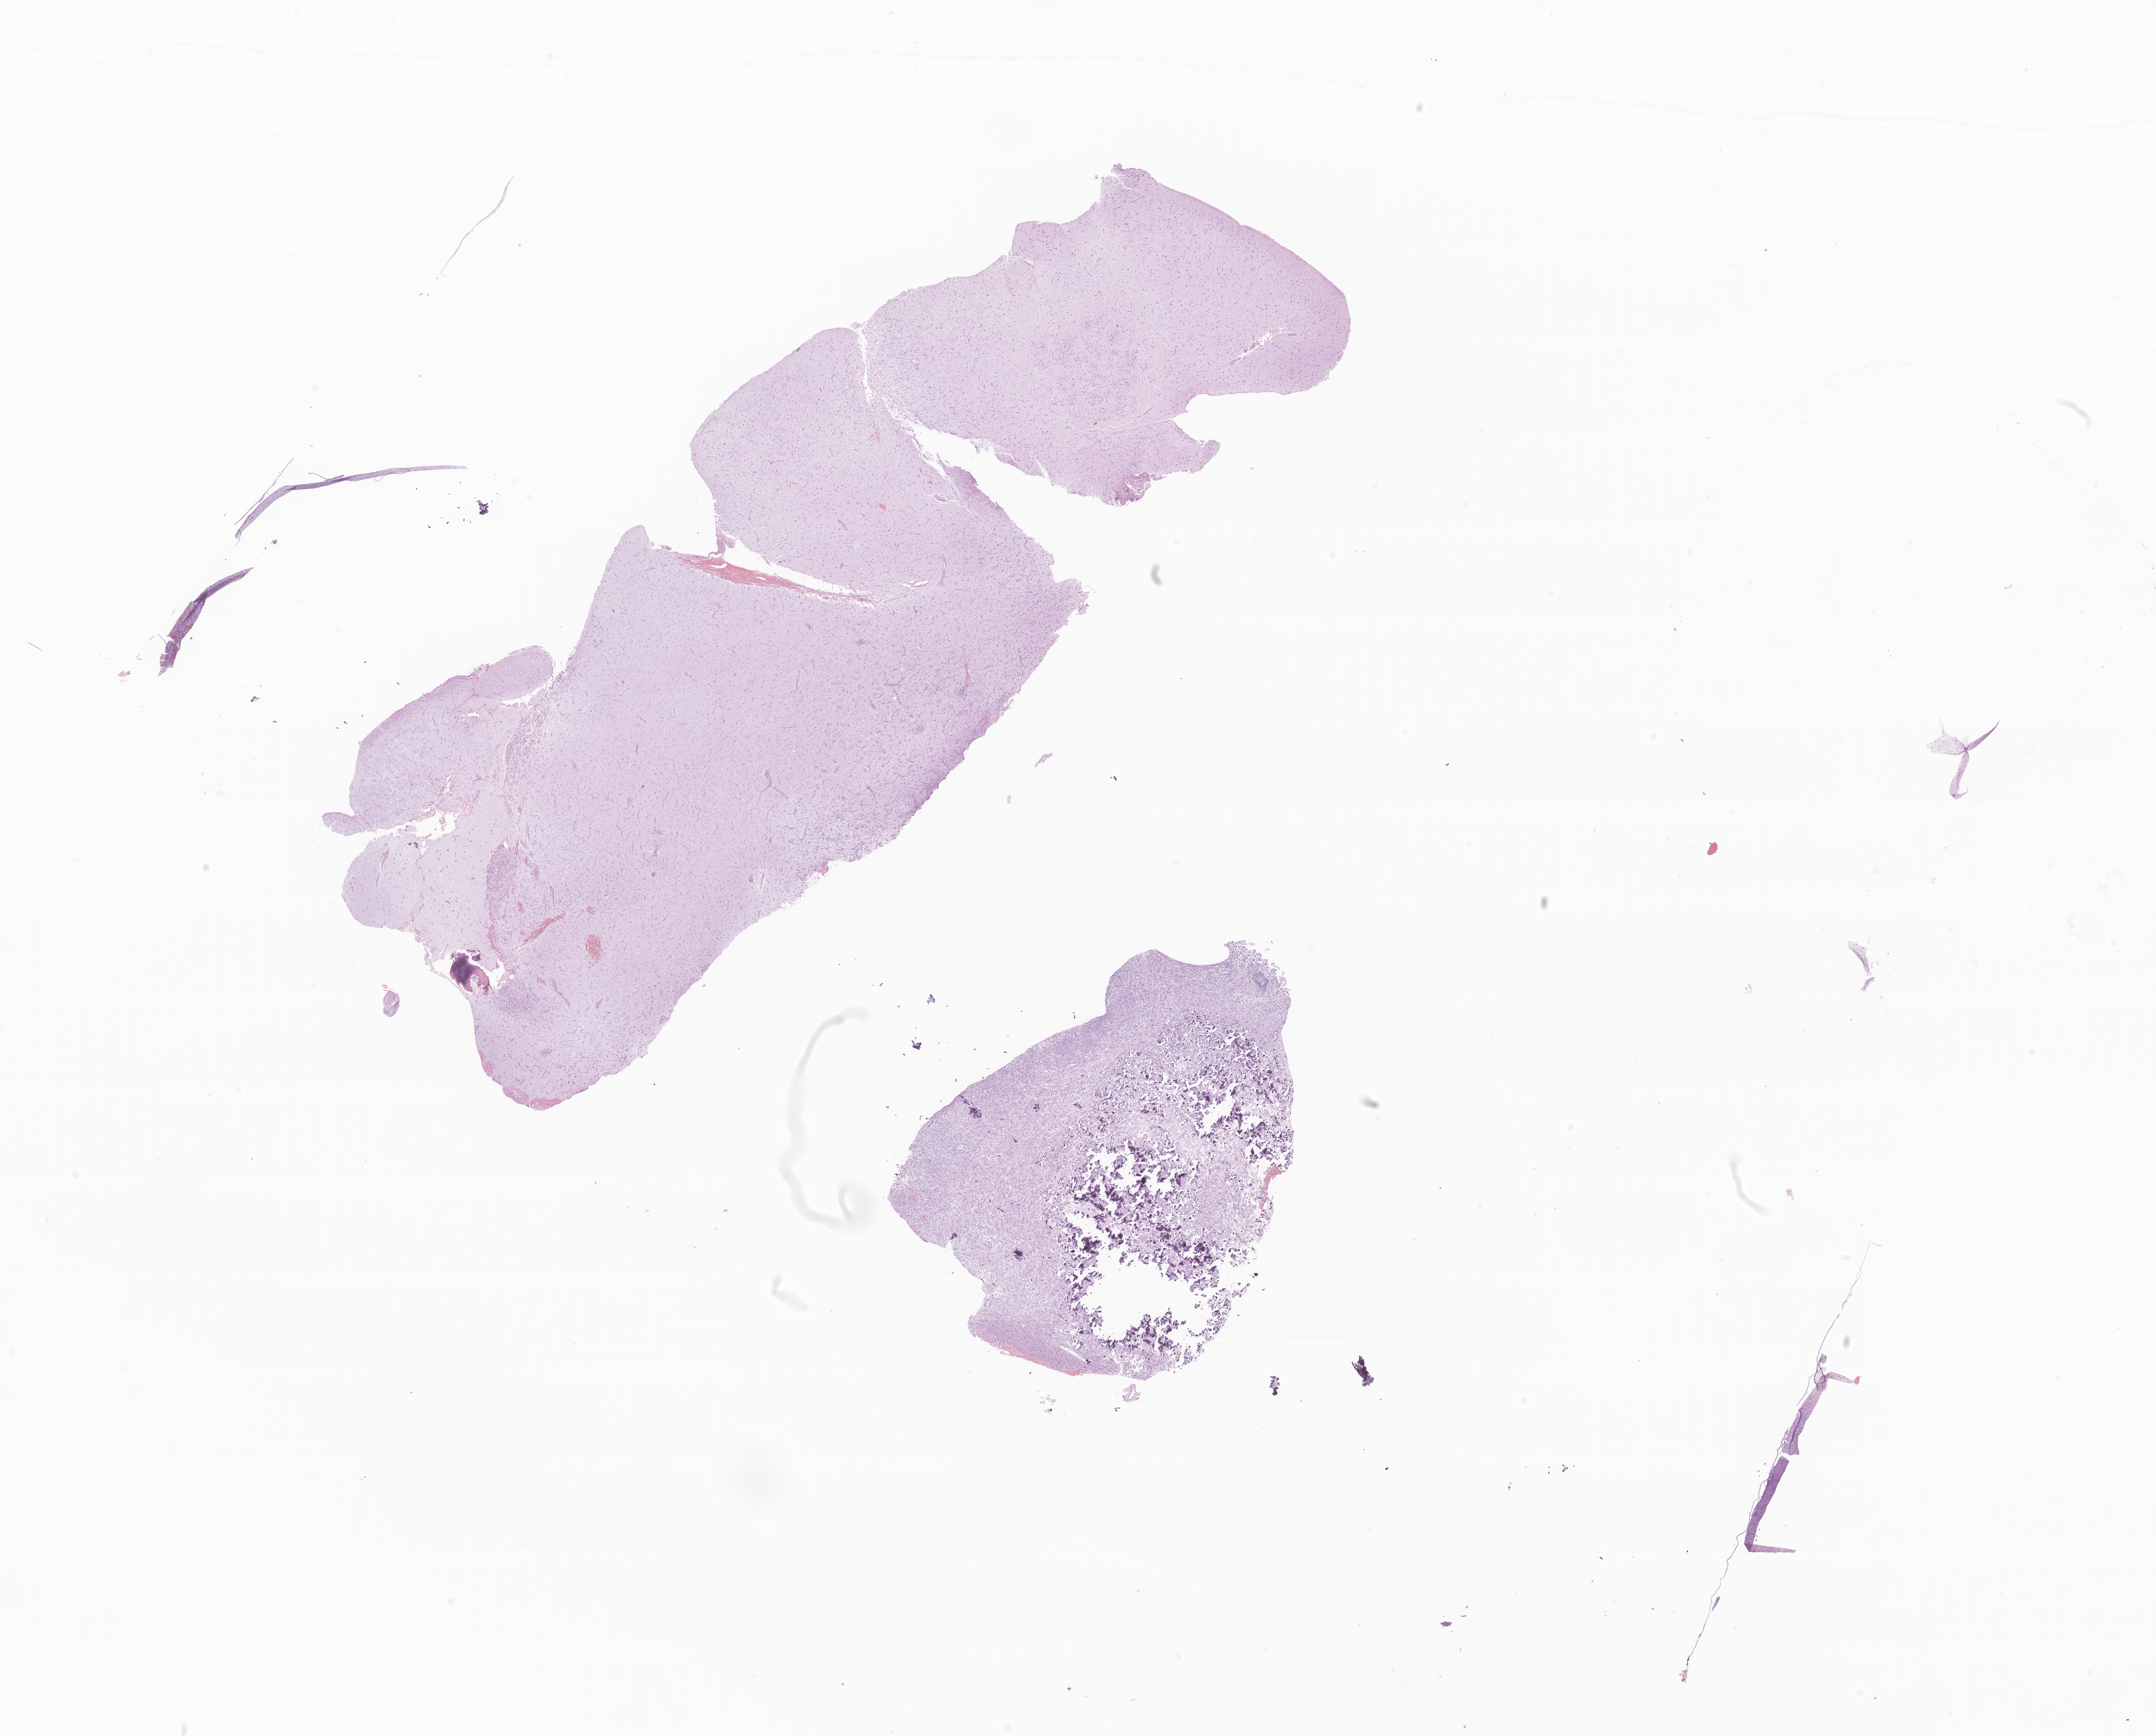
Whole-slide image, H&E stain of tumor tissue from the brain — shown as a low-resolution overview of the whole scanned area (about 24.7 x 19.9 mm); formalin-fixed, paraffin-embedded (FFPE) tissue. Patient: female, age 175 months (14 years 7 months).
Recorded diagnosis: Neoplasm, malignant.